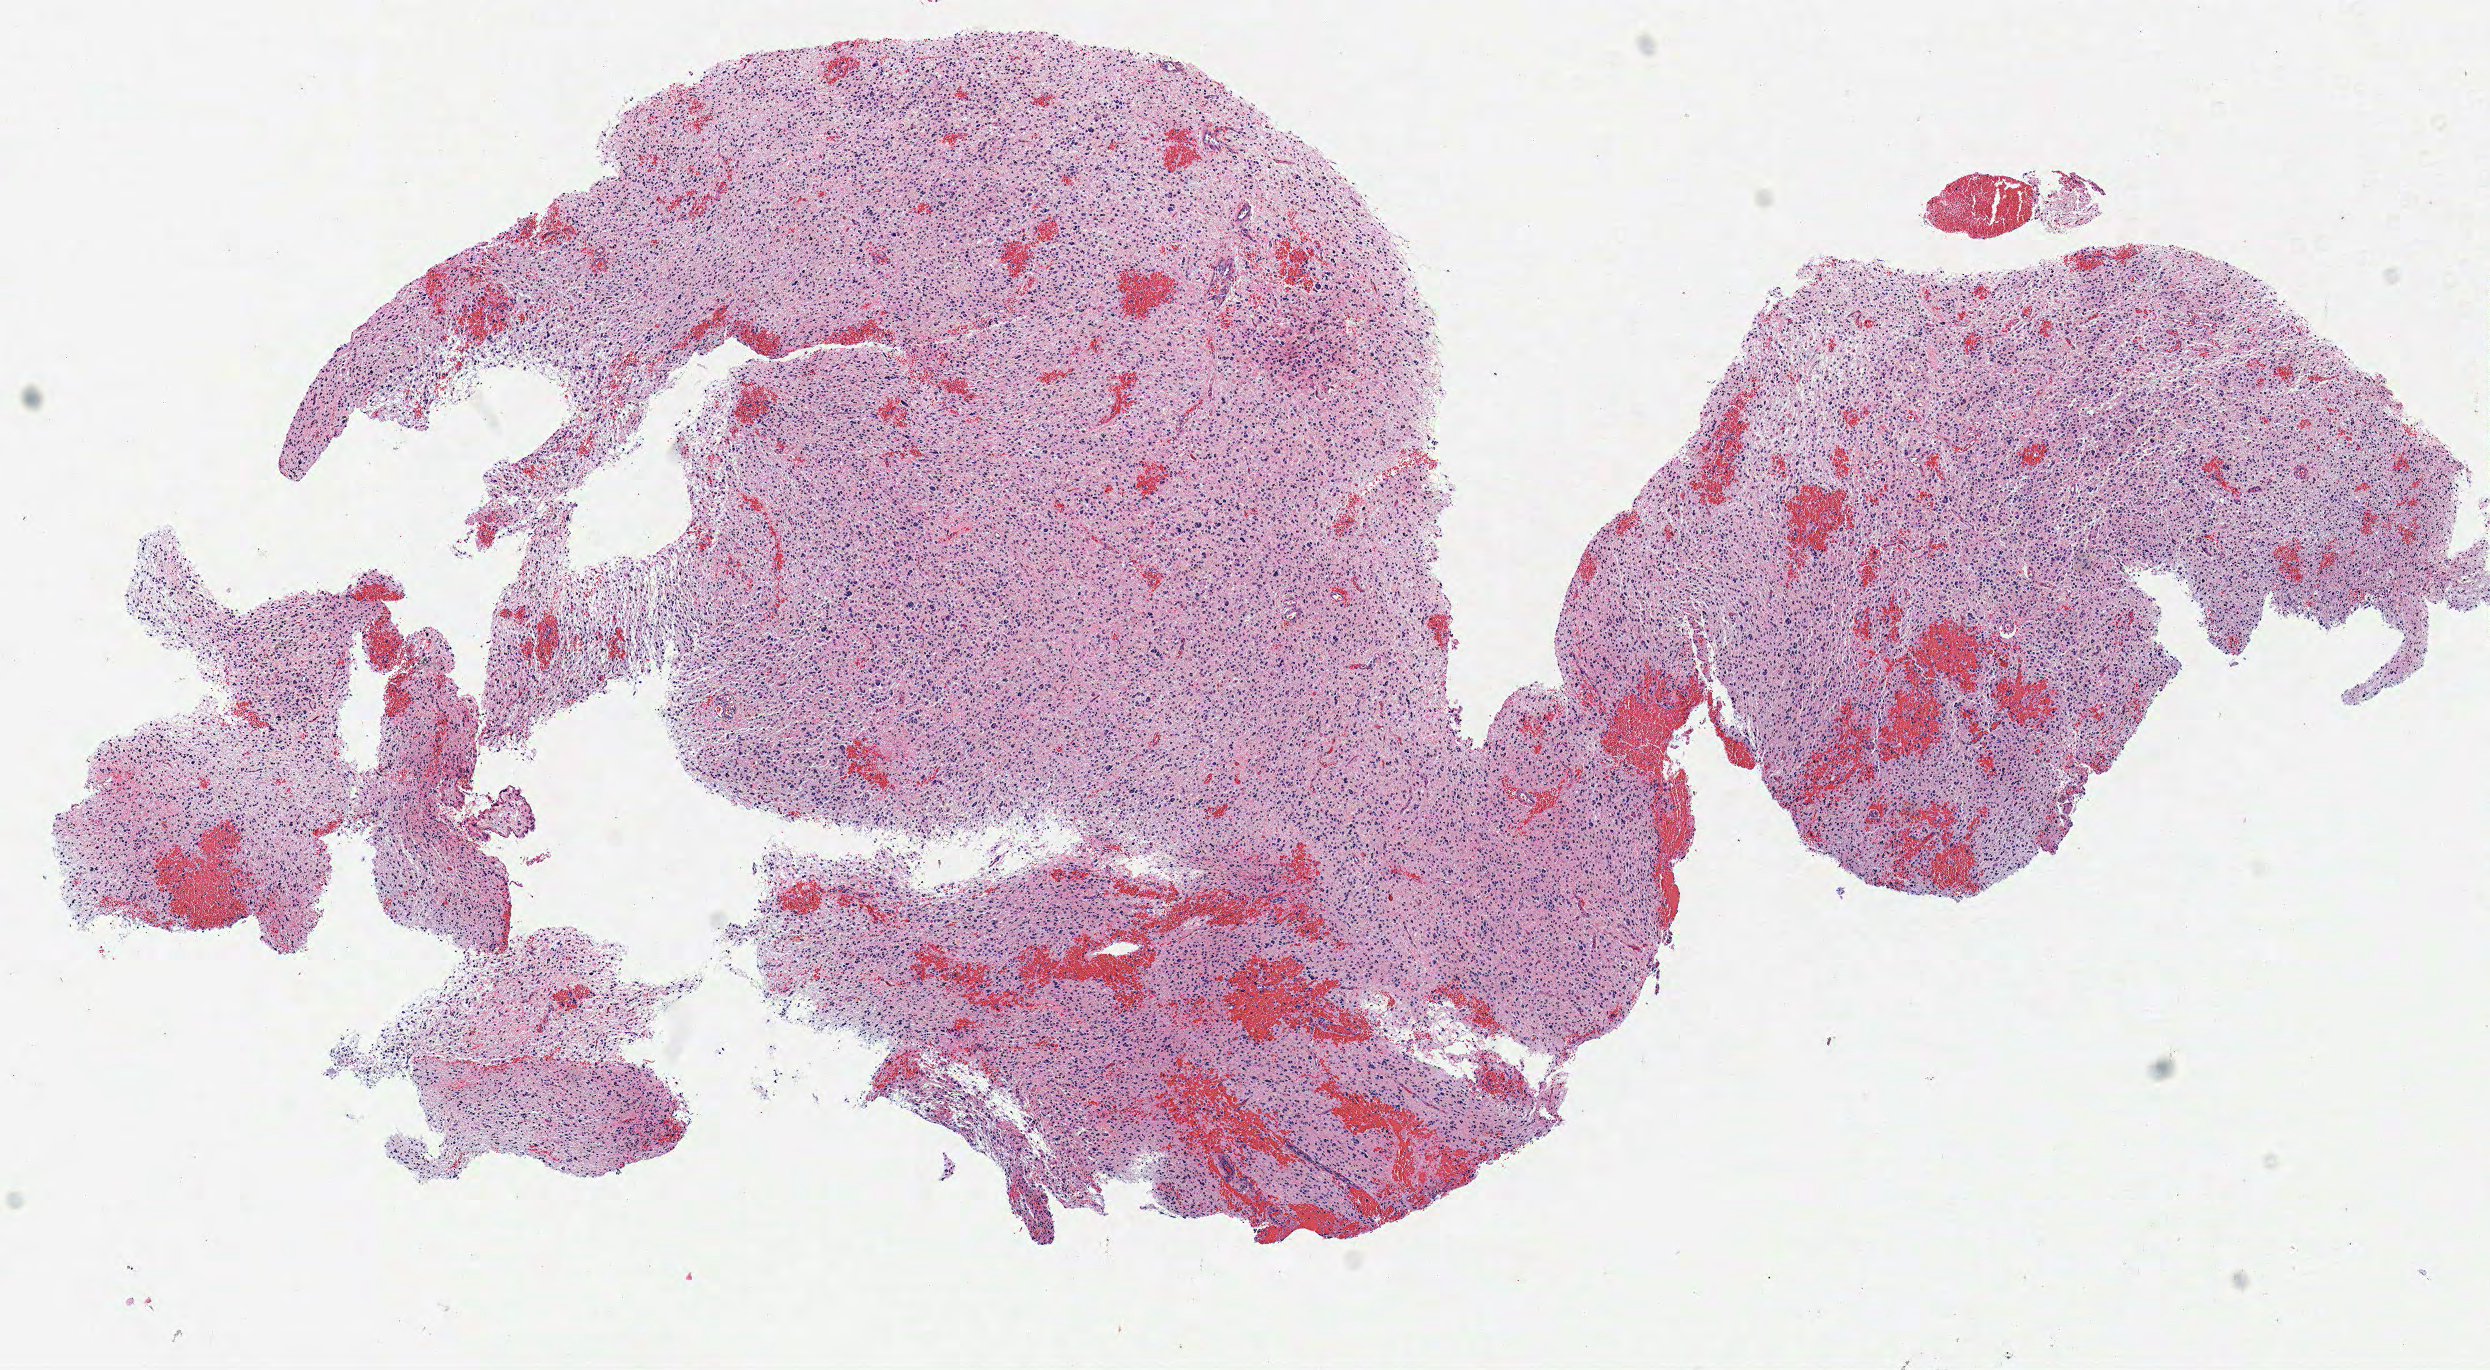
Digitized H&E tissue section (whole slide) — a low-resolution overview of the entire scanned area, about 9.8 x 5.4 mm, frozen section from the top of the tissue portion, sample: primary tumour, brain. Male patient; age at initial diagnosis 60 years. Composition of this section per pathologist review: tumour cells 100%, tumour nuclei 80%, normal cells 0%, stromal cells 0%, necrosis 0%.
Histologic diagnosis: Glioblastoma.